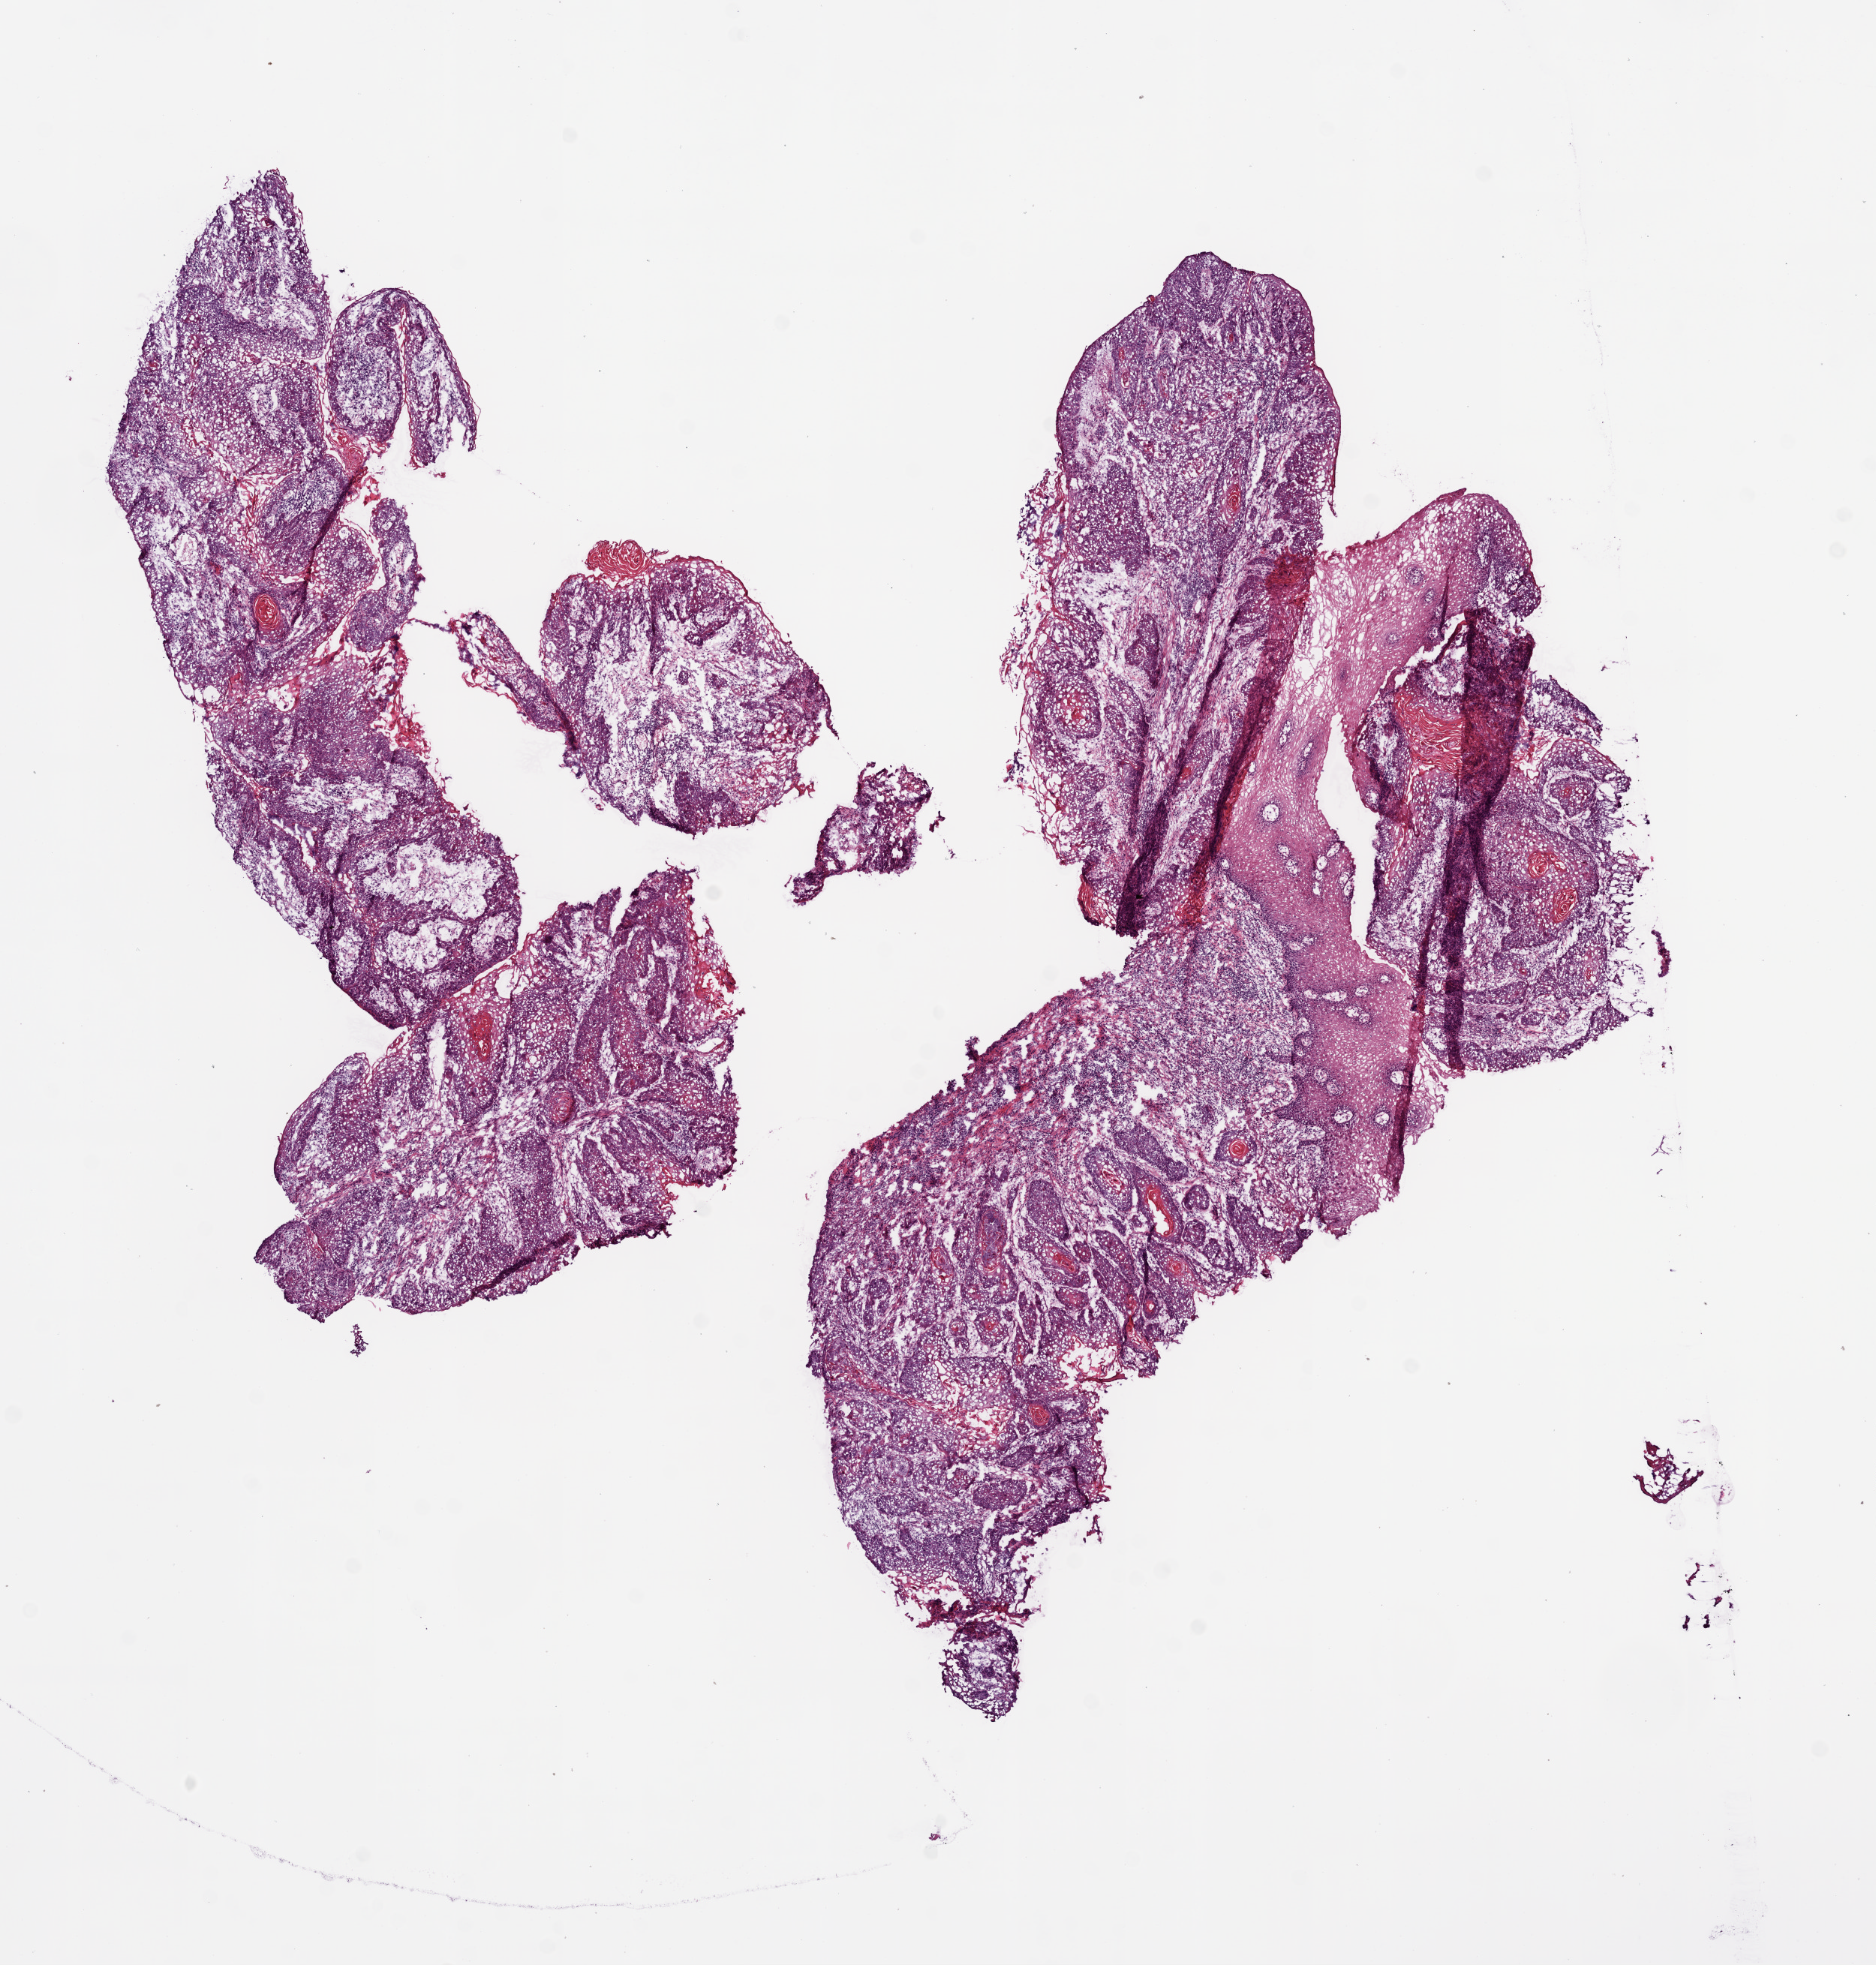
Hematoxylin and eosin (H&E) stained whole-slide image — a low-resolution overview of the entire scanned area, about 10.0 x 10.5 mm (slide scanned at 20x). Frozen section. Sample: primary tumour, head and neck. Patient: male, age at initial diagnosis 73 years. Histologic grade: G2 (moderately differentiated). Composition of this section per pathologist review: tumour cells 65%, tumour nuclei 75%, normal cells 15%, stromal cells 20%, necrosis 0%.
TNM: T2 N1. AJCC pathologic stage: III (7th edition). Pathologic diagnosis: Squamous cell carcinoma, NOS (overlapping lesion of lip, oral cavity and pharynx).